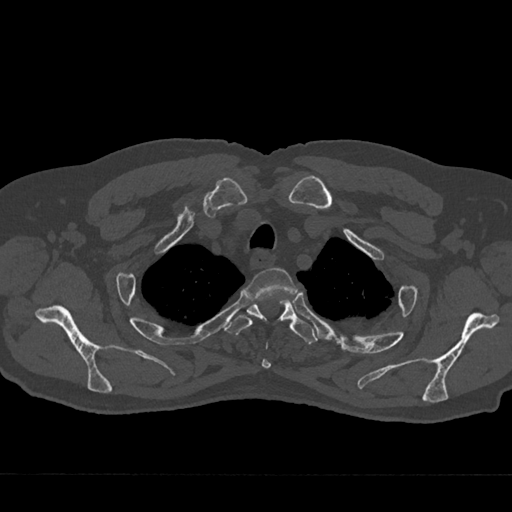
CT including the spine, one axial slice; slice 587 of 797 in the series (ordered by position); bone window (W 1800 / L 400 HU); 0.5 mm slice thickness; 512 × 512 image matrix, field of view 377 × 377 mm. Male patient, age 75 years. From the clinical record (not read from this slice): primary cancer: renal.
Structures marked on this image (semi-automatically segmented with operator editing):
- T2 vertebra: bounding box (x1, y1, x2, y2) in pixels: (248, 268, 297, 369)
- T3 vertebra: (226, 297, 318, 345)